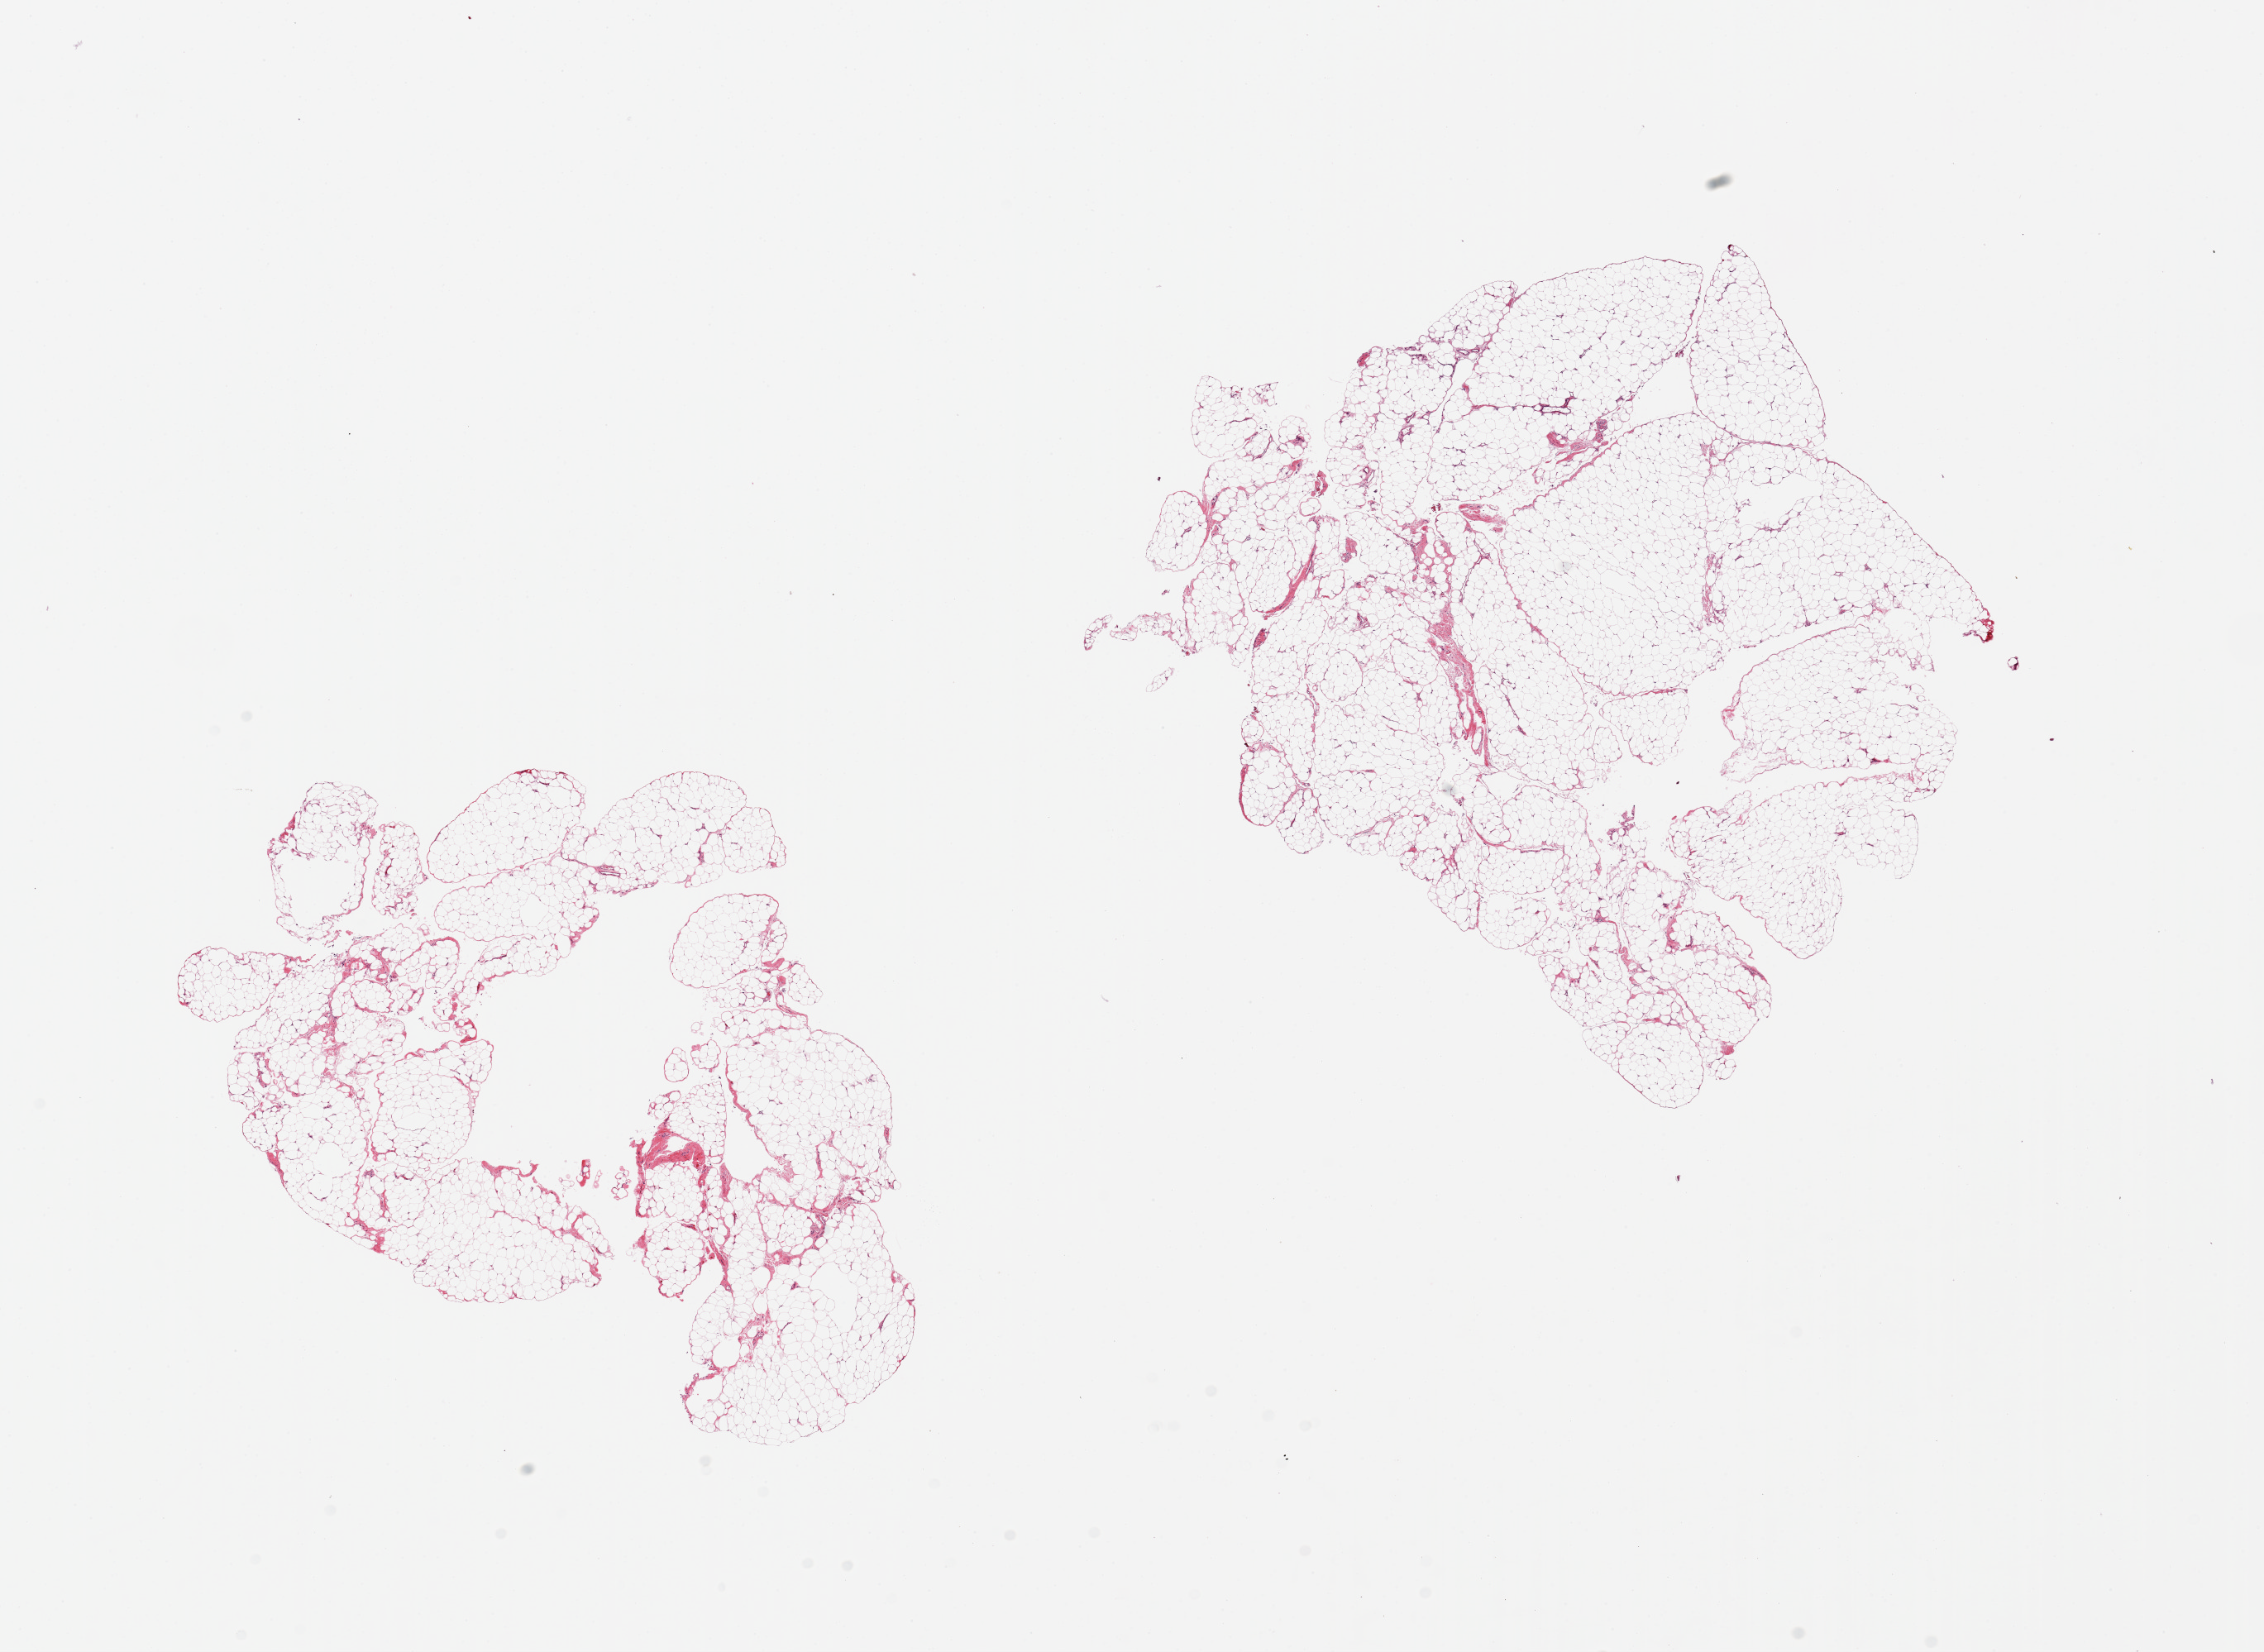
Digitized H&E-stained section — shown as a low-resolution overview of the whole scanned area (about 21.7 x 15.8 mm); PAXgene-fixed, paraffin-embedded tissue; target tissue: omentum; donor tissue sample.
Pathologist's review note for this sample: 2 pieces.